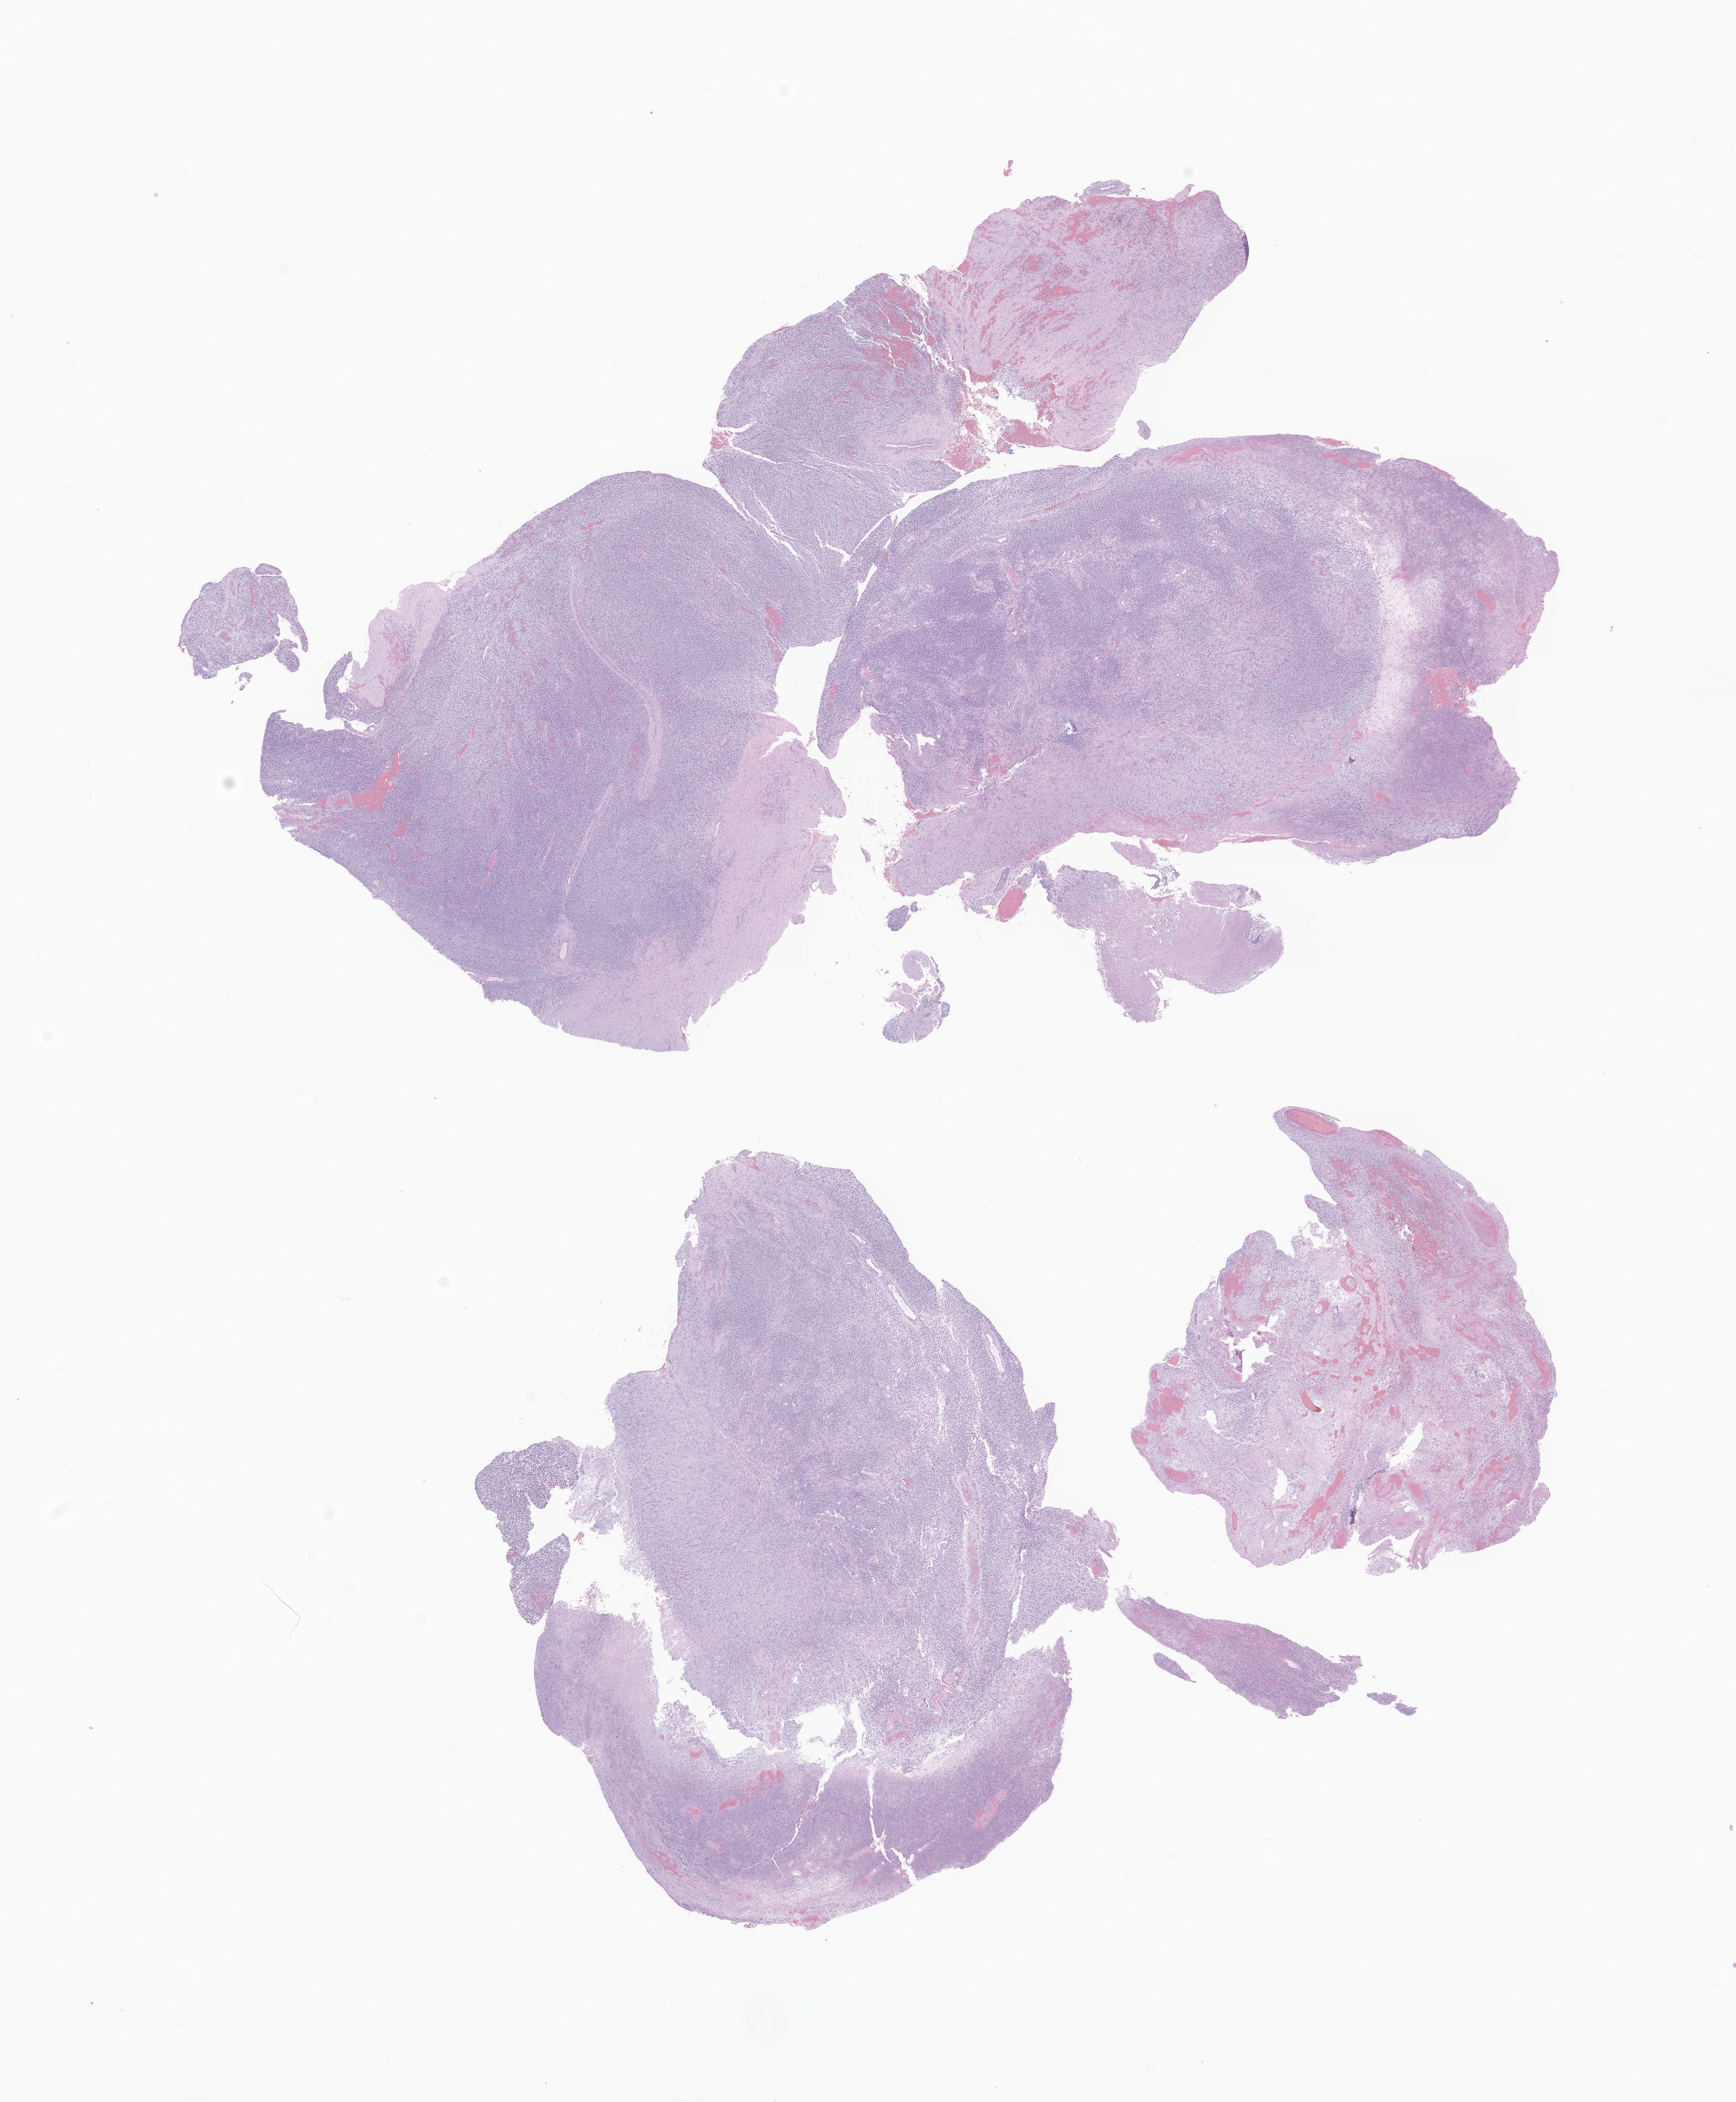
H&E whole-slide image of tumor tissue from the nasopharynx — shown as a low-resolution overview of the whole scanned area (about 18.0 x 21.8 mm). Formalin-fixed, paraffin-embedded (FFPE) tissue. Patient male; age 86 months (7 years 2 months).
Diagnosis (ICD-O-3 morphology term): Embryonal rhabdomyosarcoma, NOS.